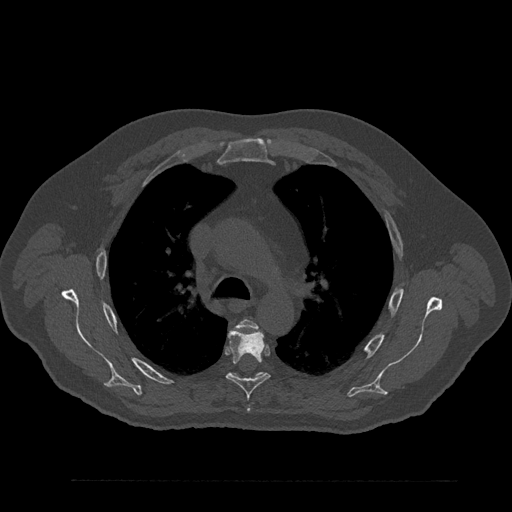
CT including the spine, one axial slice; position 602 of 797 along the scan axis; reconstruction kernel Br40s/3; 120 kVp; bone window (W 1800 / L 400 HU); 0.5 mm slice thickness; 512 × 512 image matrix, field of view 430 × 430 mm. Patient: male, 61 years. Case-level facts recorded for this patient, not image findings: primary cancer: prostate.
Structures marked on this image (semi-automatically segmented with operator editing):
- T4 vertebra: box from (x=238, y=319) to (x=257, y=411) px
- T5 vertebra: (x=226, y=329)–(x=270, y=400)
- T6 vertebra: (x=230, y=372)–(x=266, y=380)